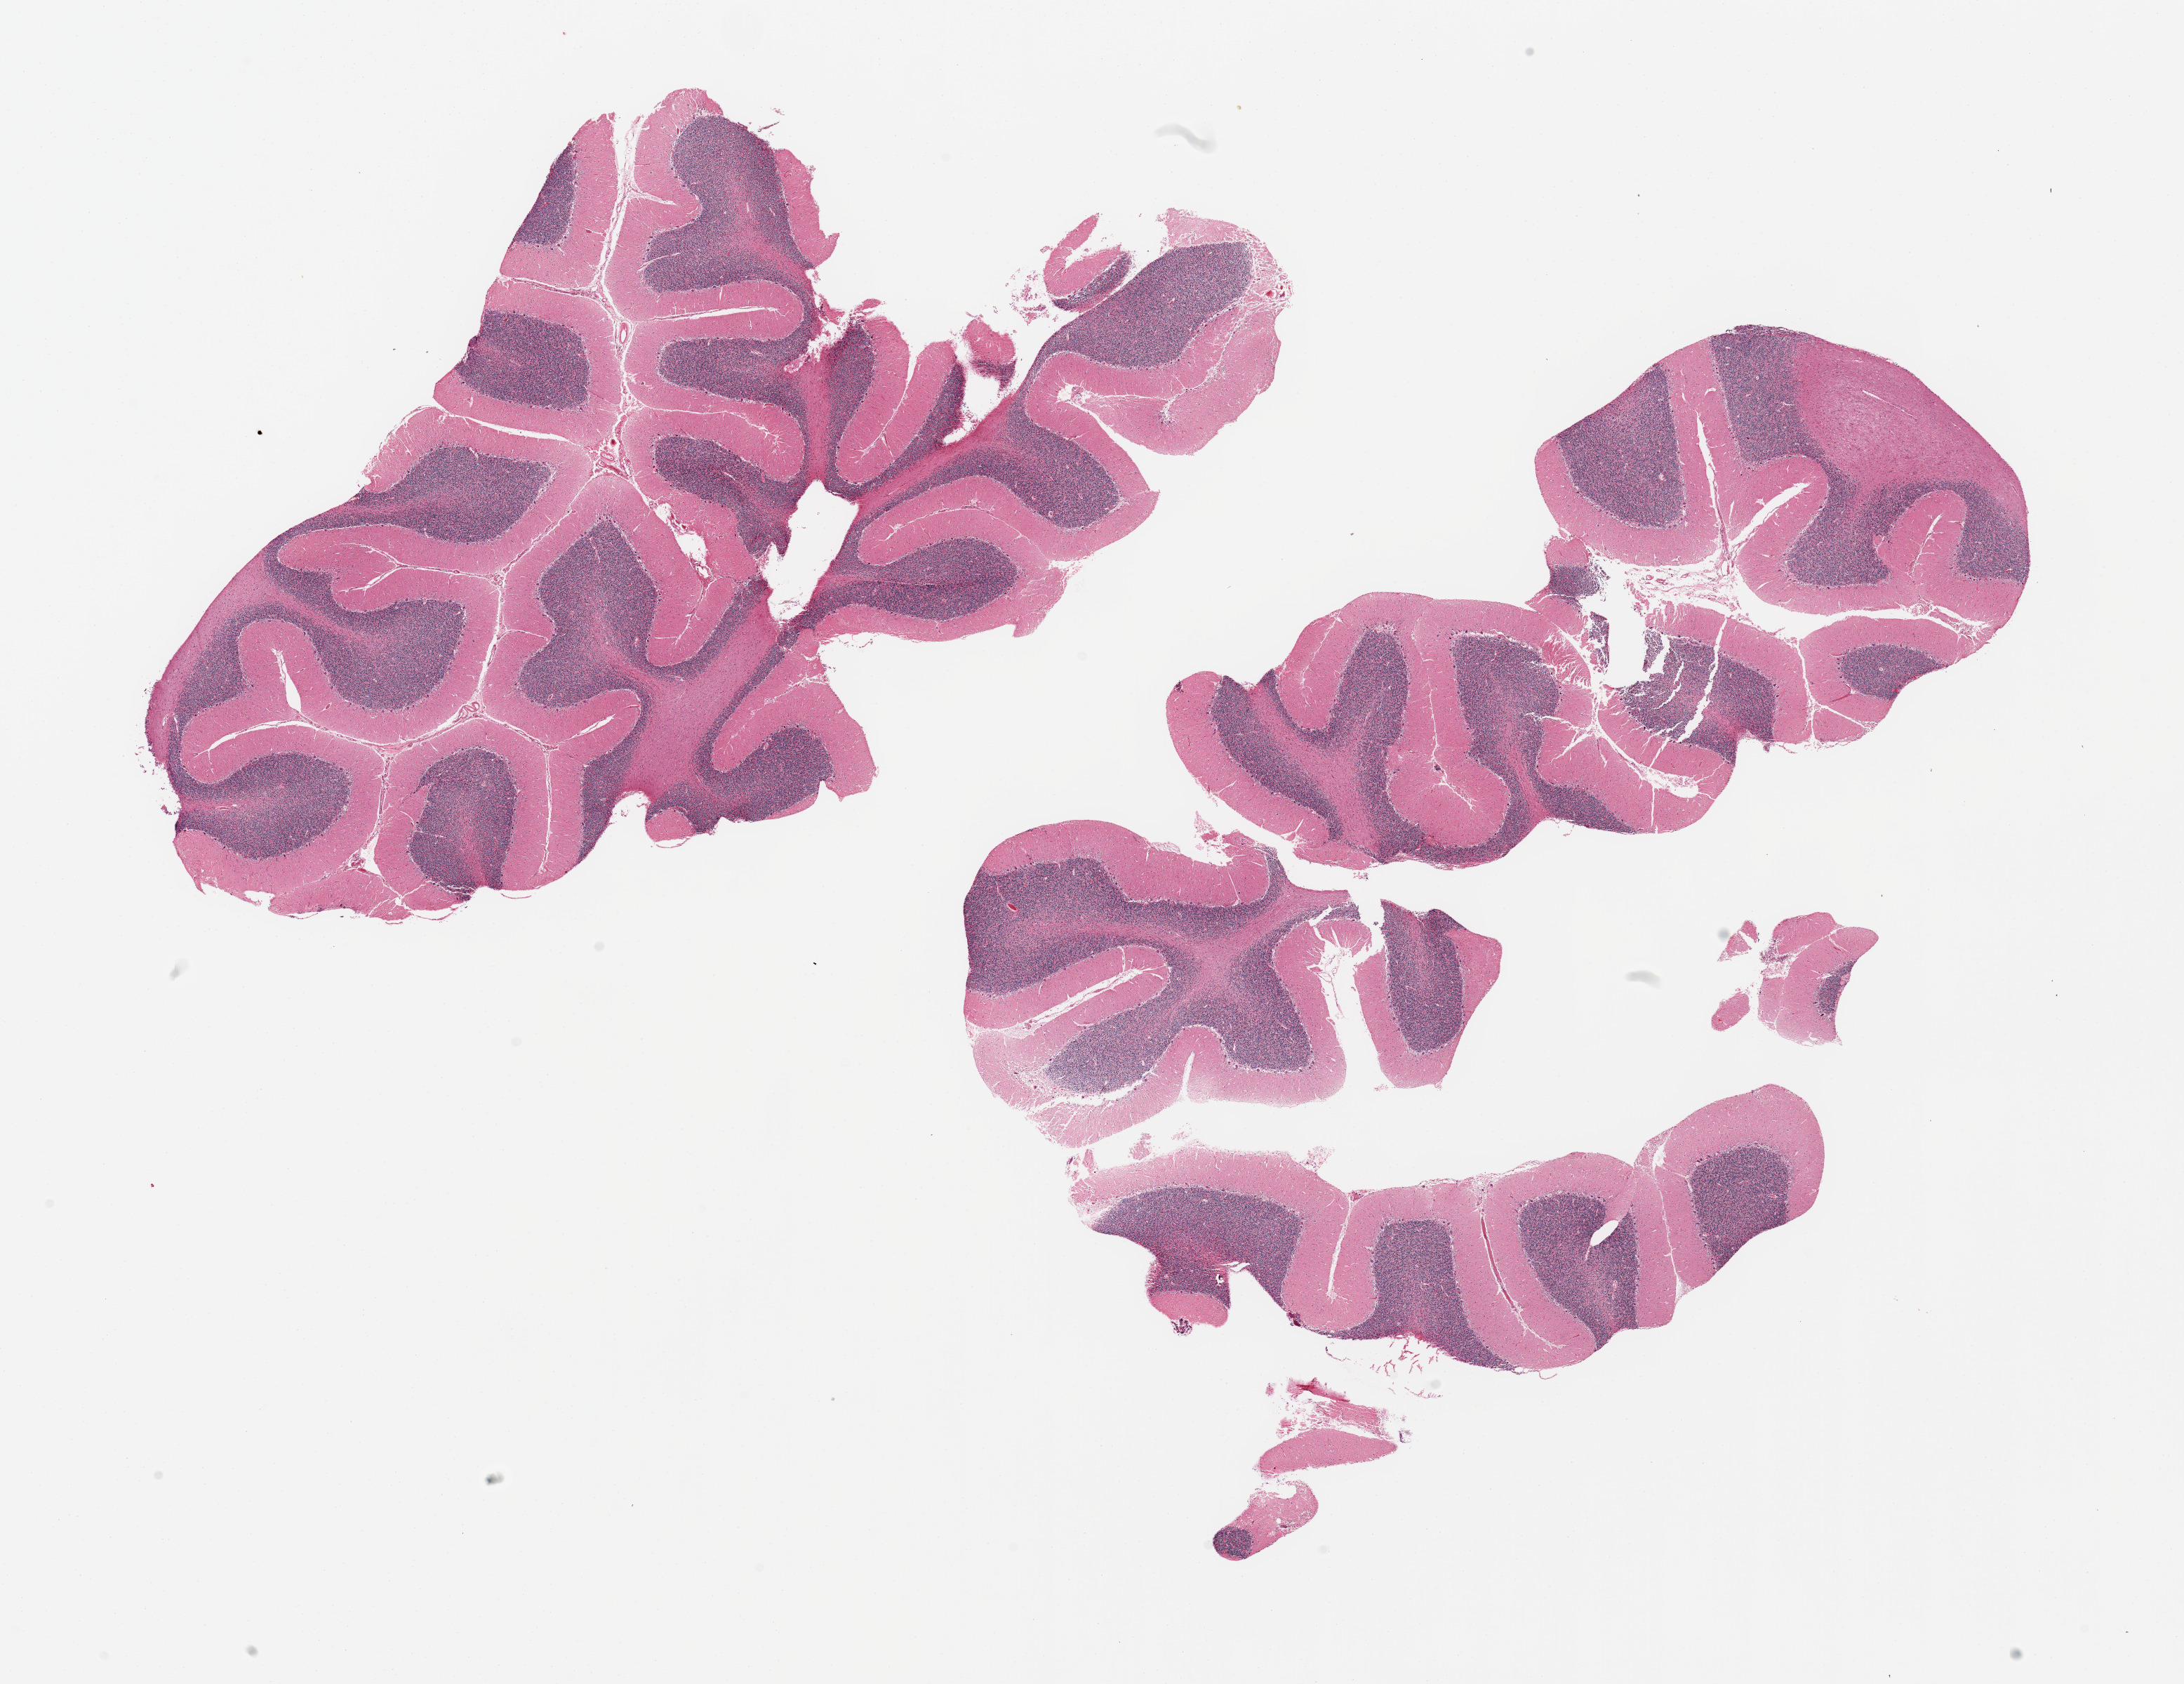
Whole-slide image, hematoxylin and eosin (H&E) stain, shown as a low-resolution overview of the whole scanned area (about 24.6 x 19.0 mm, acquisition: 20x scan), PAXgene-fixed paraffin-embedded (PFPE) section, section of cerebellum (target tissue), tissue donor sample.
Reviewer comment on this tissue sample: 2 pieces, no abnormalities.